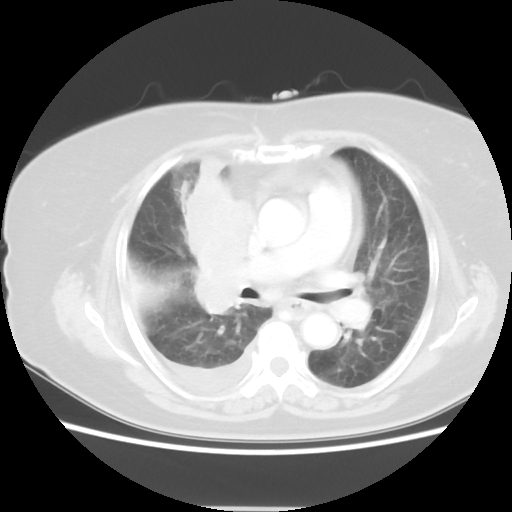
Chest CT, one axial slice. Slice 29 of 48 in the series (ordered by position). Reconstruction kernel STANDARD. Lung window (W 1500 / L -600 HU). 5 mm slice thickness. 512 × 512 image matrix, field of view 360 × 360 mm. Female patient, age 73 years. Case-level facts recorded for this patient, not image findings: clinical TNM (as recorded): T3 N3 M1b.
Structures marked on this image (bounding box drawn by a radiologist):
- lung tumour (recorded histology: small cell carcinoma): bounding box <184,158,250,319> (left, top, right, bottom; pixels)